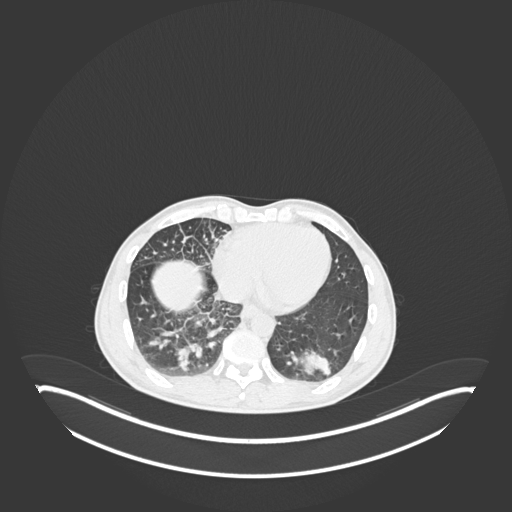
Chest CT, one axial slice; slice 68 of 237 in the series (ordered by position); lung window (W 1500 / L -600 HU); 1 mm slice thickness; 512 × 512 image matrix, field of view 500 × 500 mm. Male patient, age 49 years. From the clinical record (not read from this slice): clinical TNM (as recorded): T2b N1 M0.
Annotated regions visible in this slice (bounding box drawn by a radiologist):
- lung tumour (recorded histology: adenocarcinoma): box from (x=294, y=343) to (x=336, y=378) px